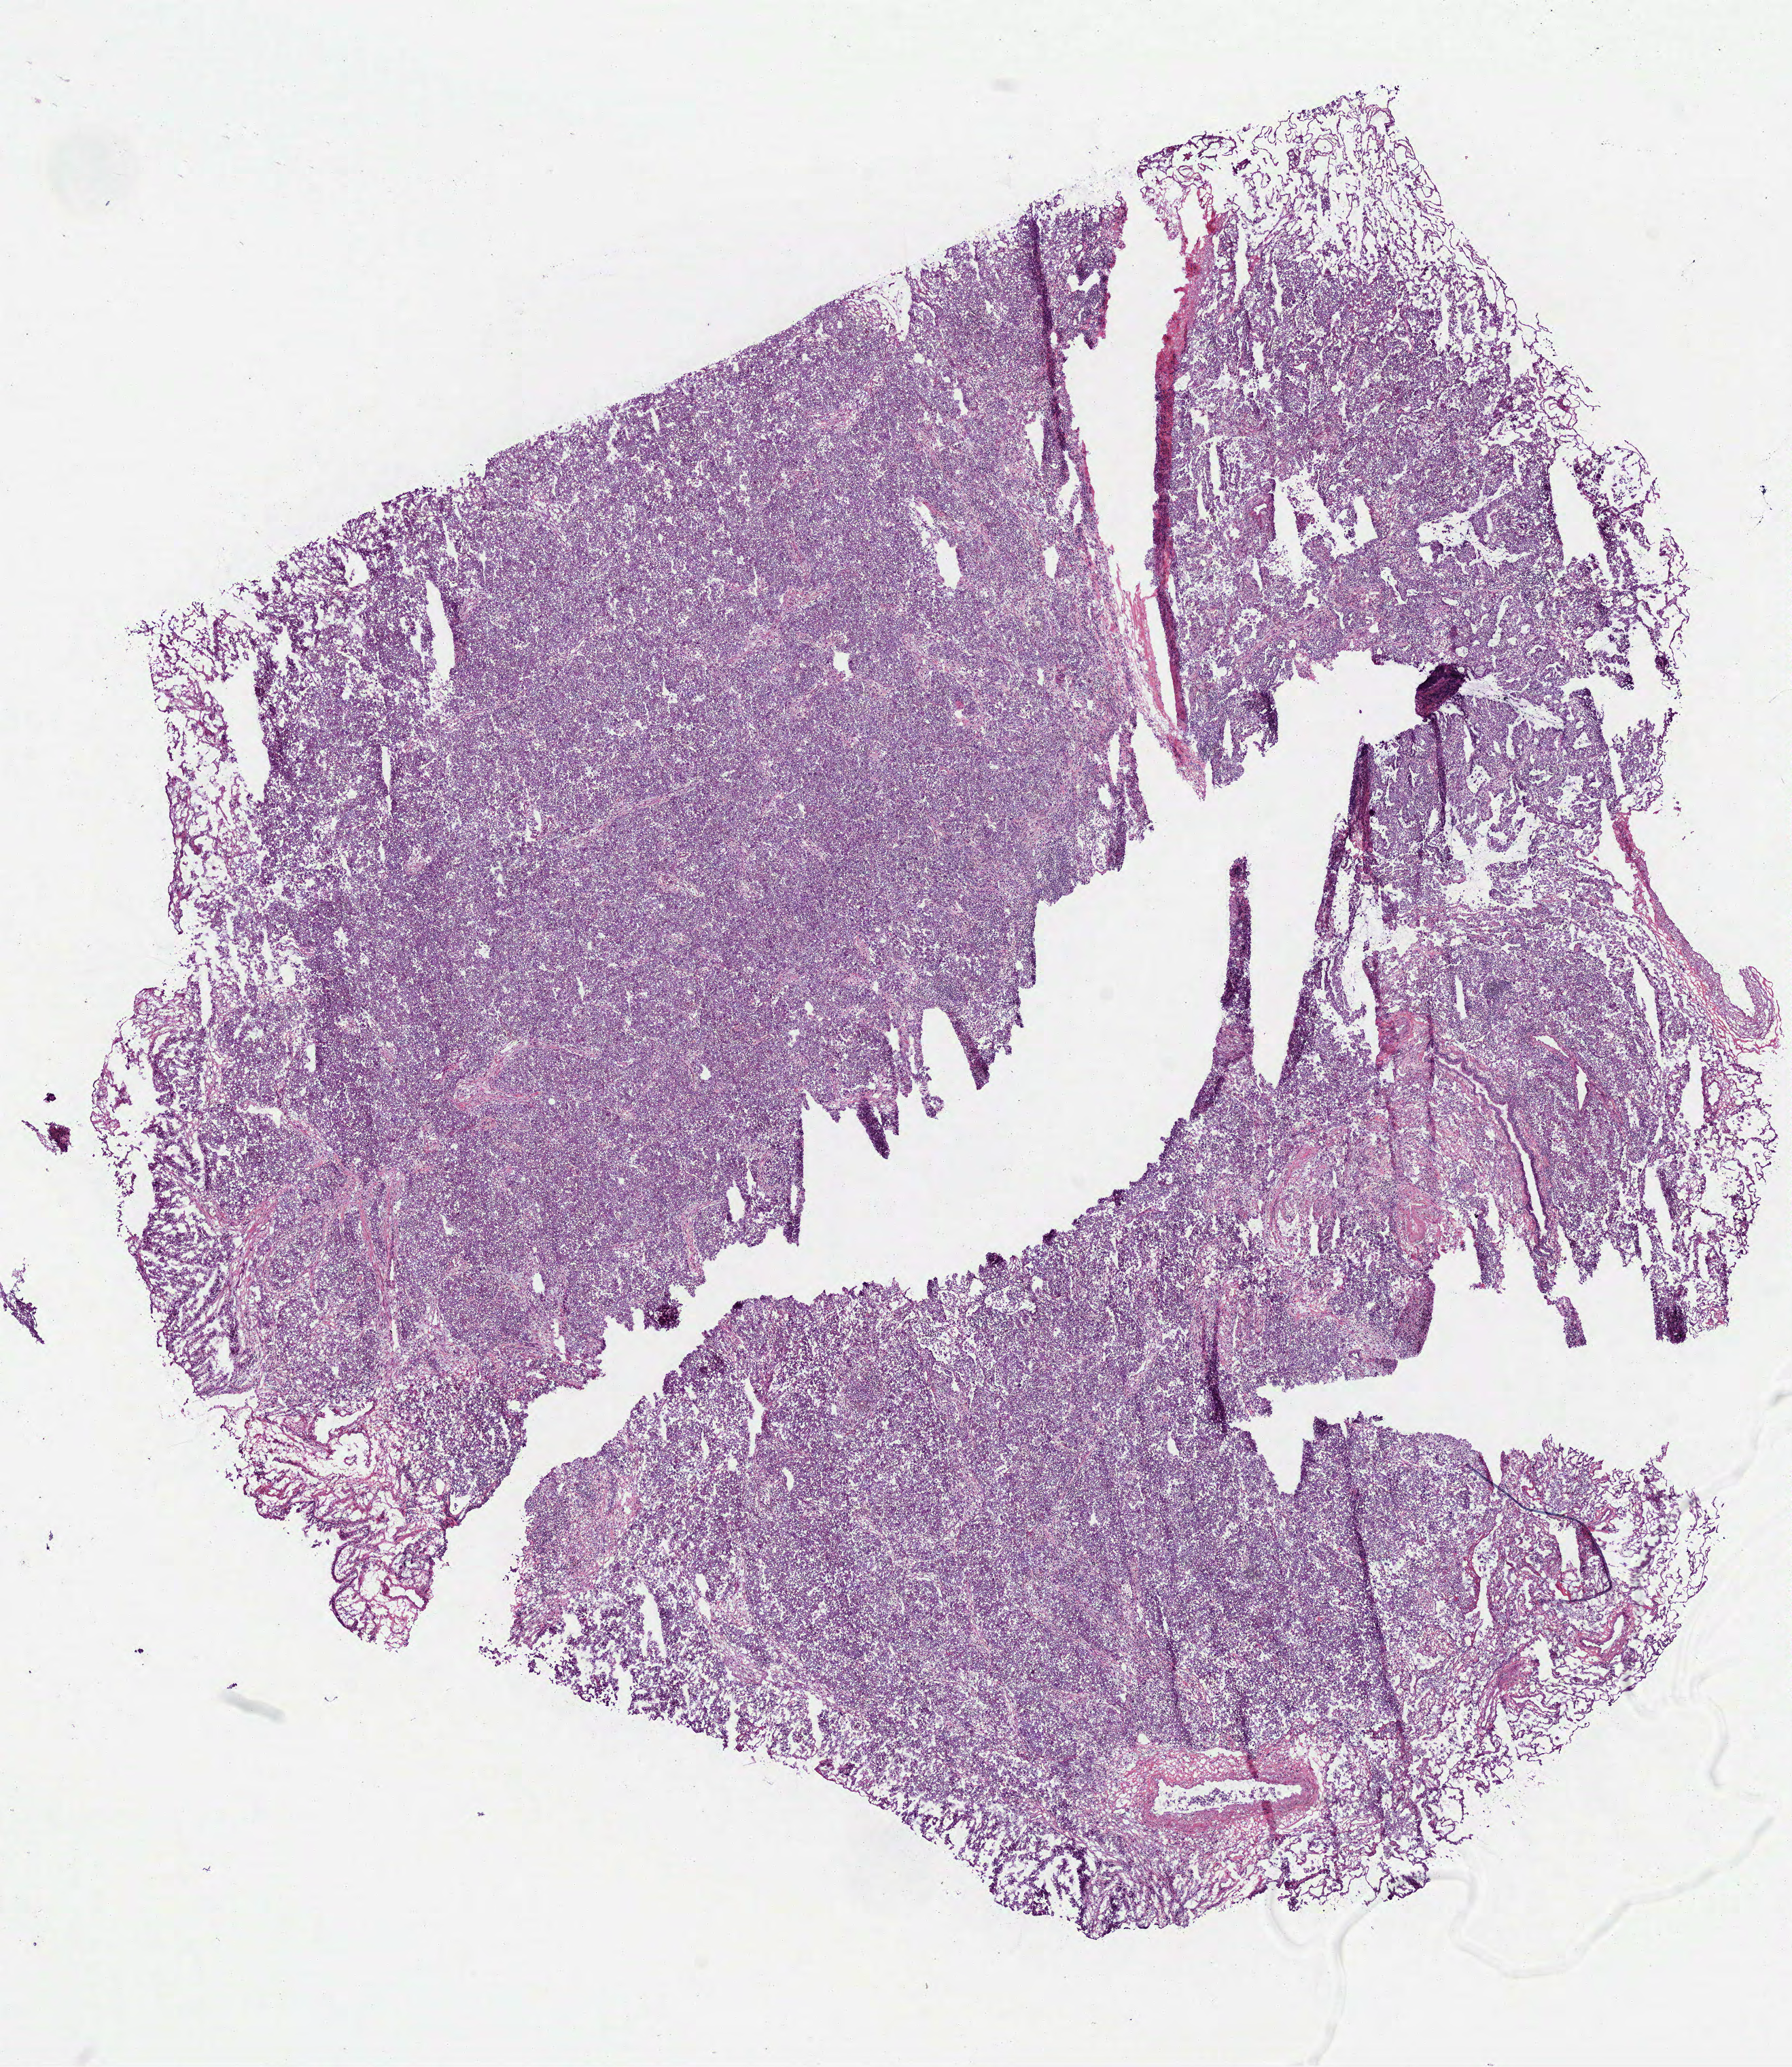
Digitized Hematoxylin and eosin (H&E) stained tissue section (whole slide), whole scanned area (about 10.6 x 12.3 mm) shown as a low-resolution overview; frozen section; sample: primary tumour, lung. Patient: female, age at initial diagnosis 68 years. Pathologist review of this section (percent, as recorded): tumour cells 87%, tumour nuclei 75%, normal cells 5%, stromal cells 5%, necrosis 3%.
• AJCC pathologic stage: IB (7th edition)
• histologic diagnosis: Bronchiolo-alveolar adenocarcinoma, NOS (lower lobe, lung)